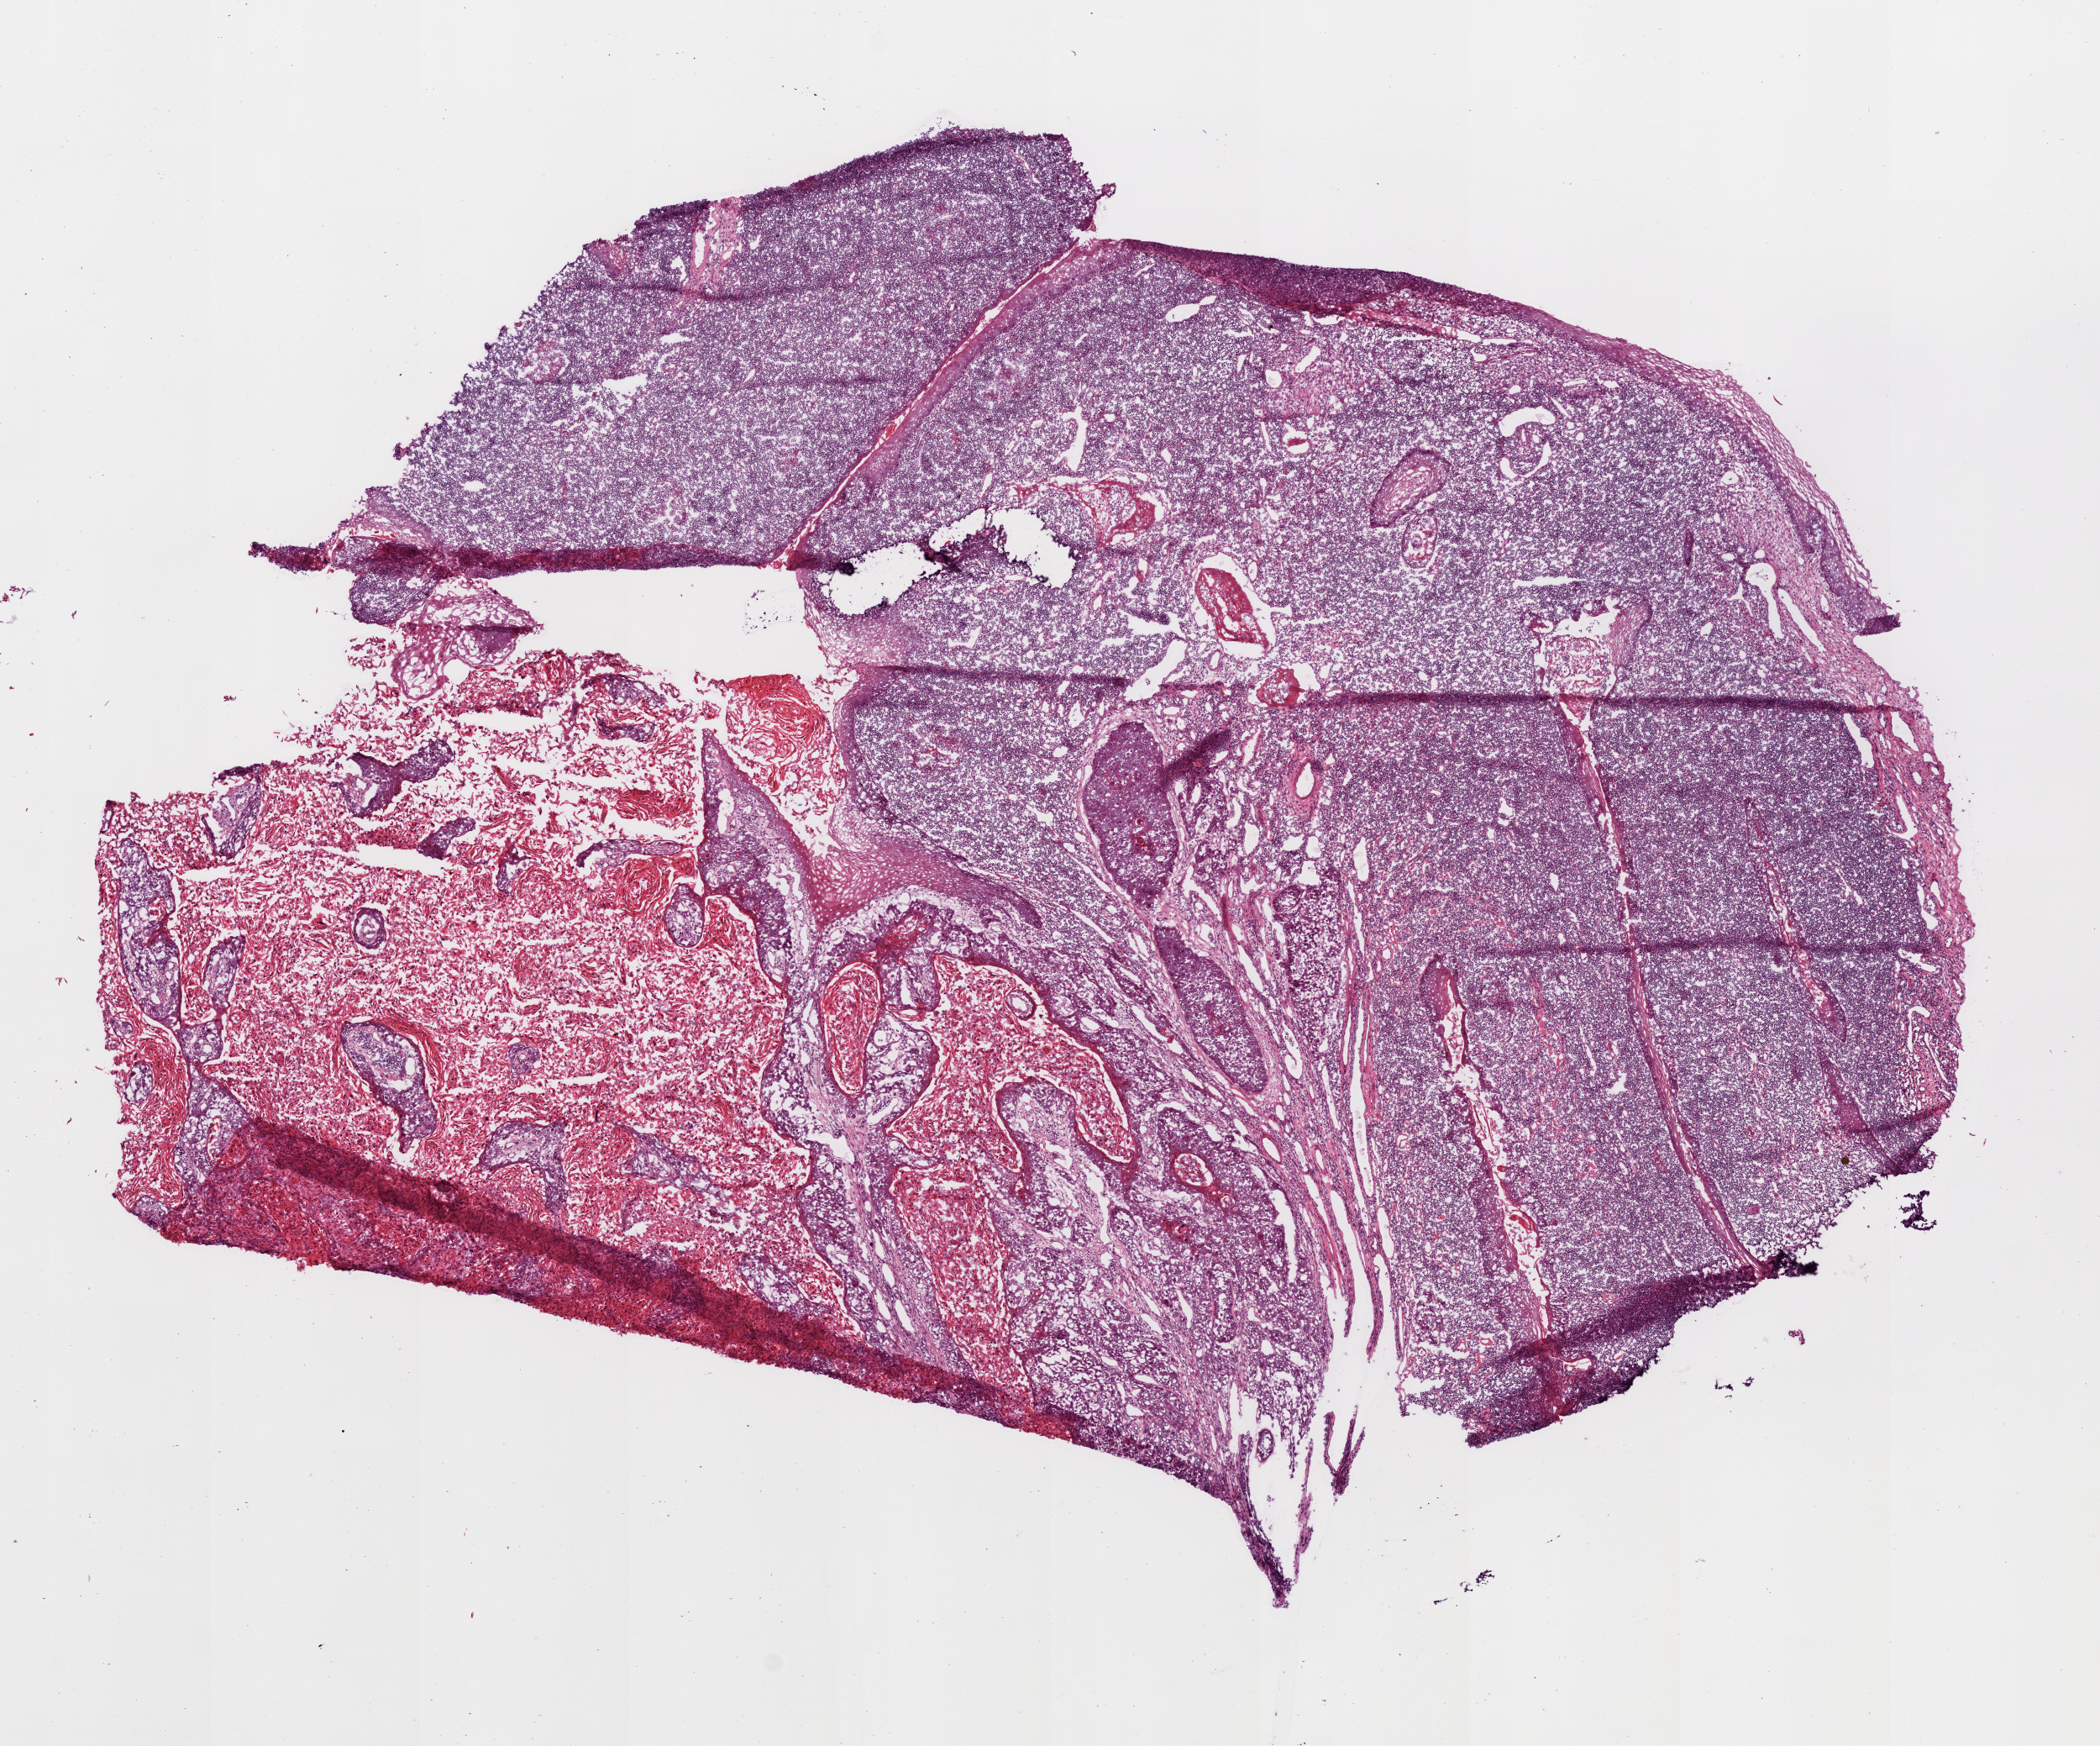
Whole-slide histology image, H&E, a low-resolution overview of the entire scanned area, about 10.0 x 8.3 mm (slide scanned at 20x). Frozen section from the bottom of the tissue portion. Head and neck, primary tumour sample. Patient: male, age at initial diagnosis 68 years. Histologic grade: G3 (poorly differentiated). Pathologist review of this section (percent, as recorded): tumour cells 24%, tumour nuclei 30%, normal cells 6%, stromal cells 49%, necrosis 21%. Infiltration values recorded for this section: lymphocyte infiltration 60%.
* histologic diagnosis: Squamous cell carcinoma, NOS (larynx, NOS)
* AJCC pathologic stage: IVA (7th edition)